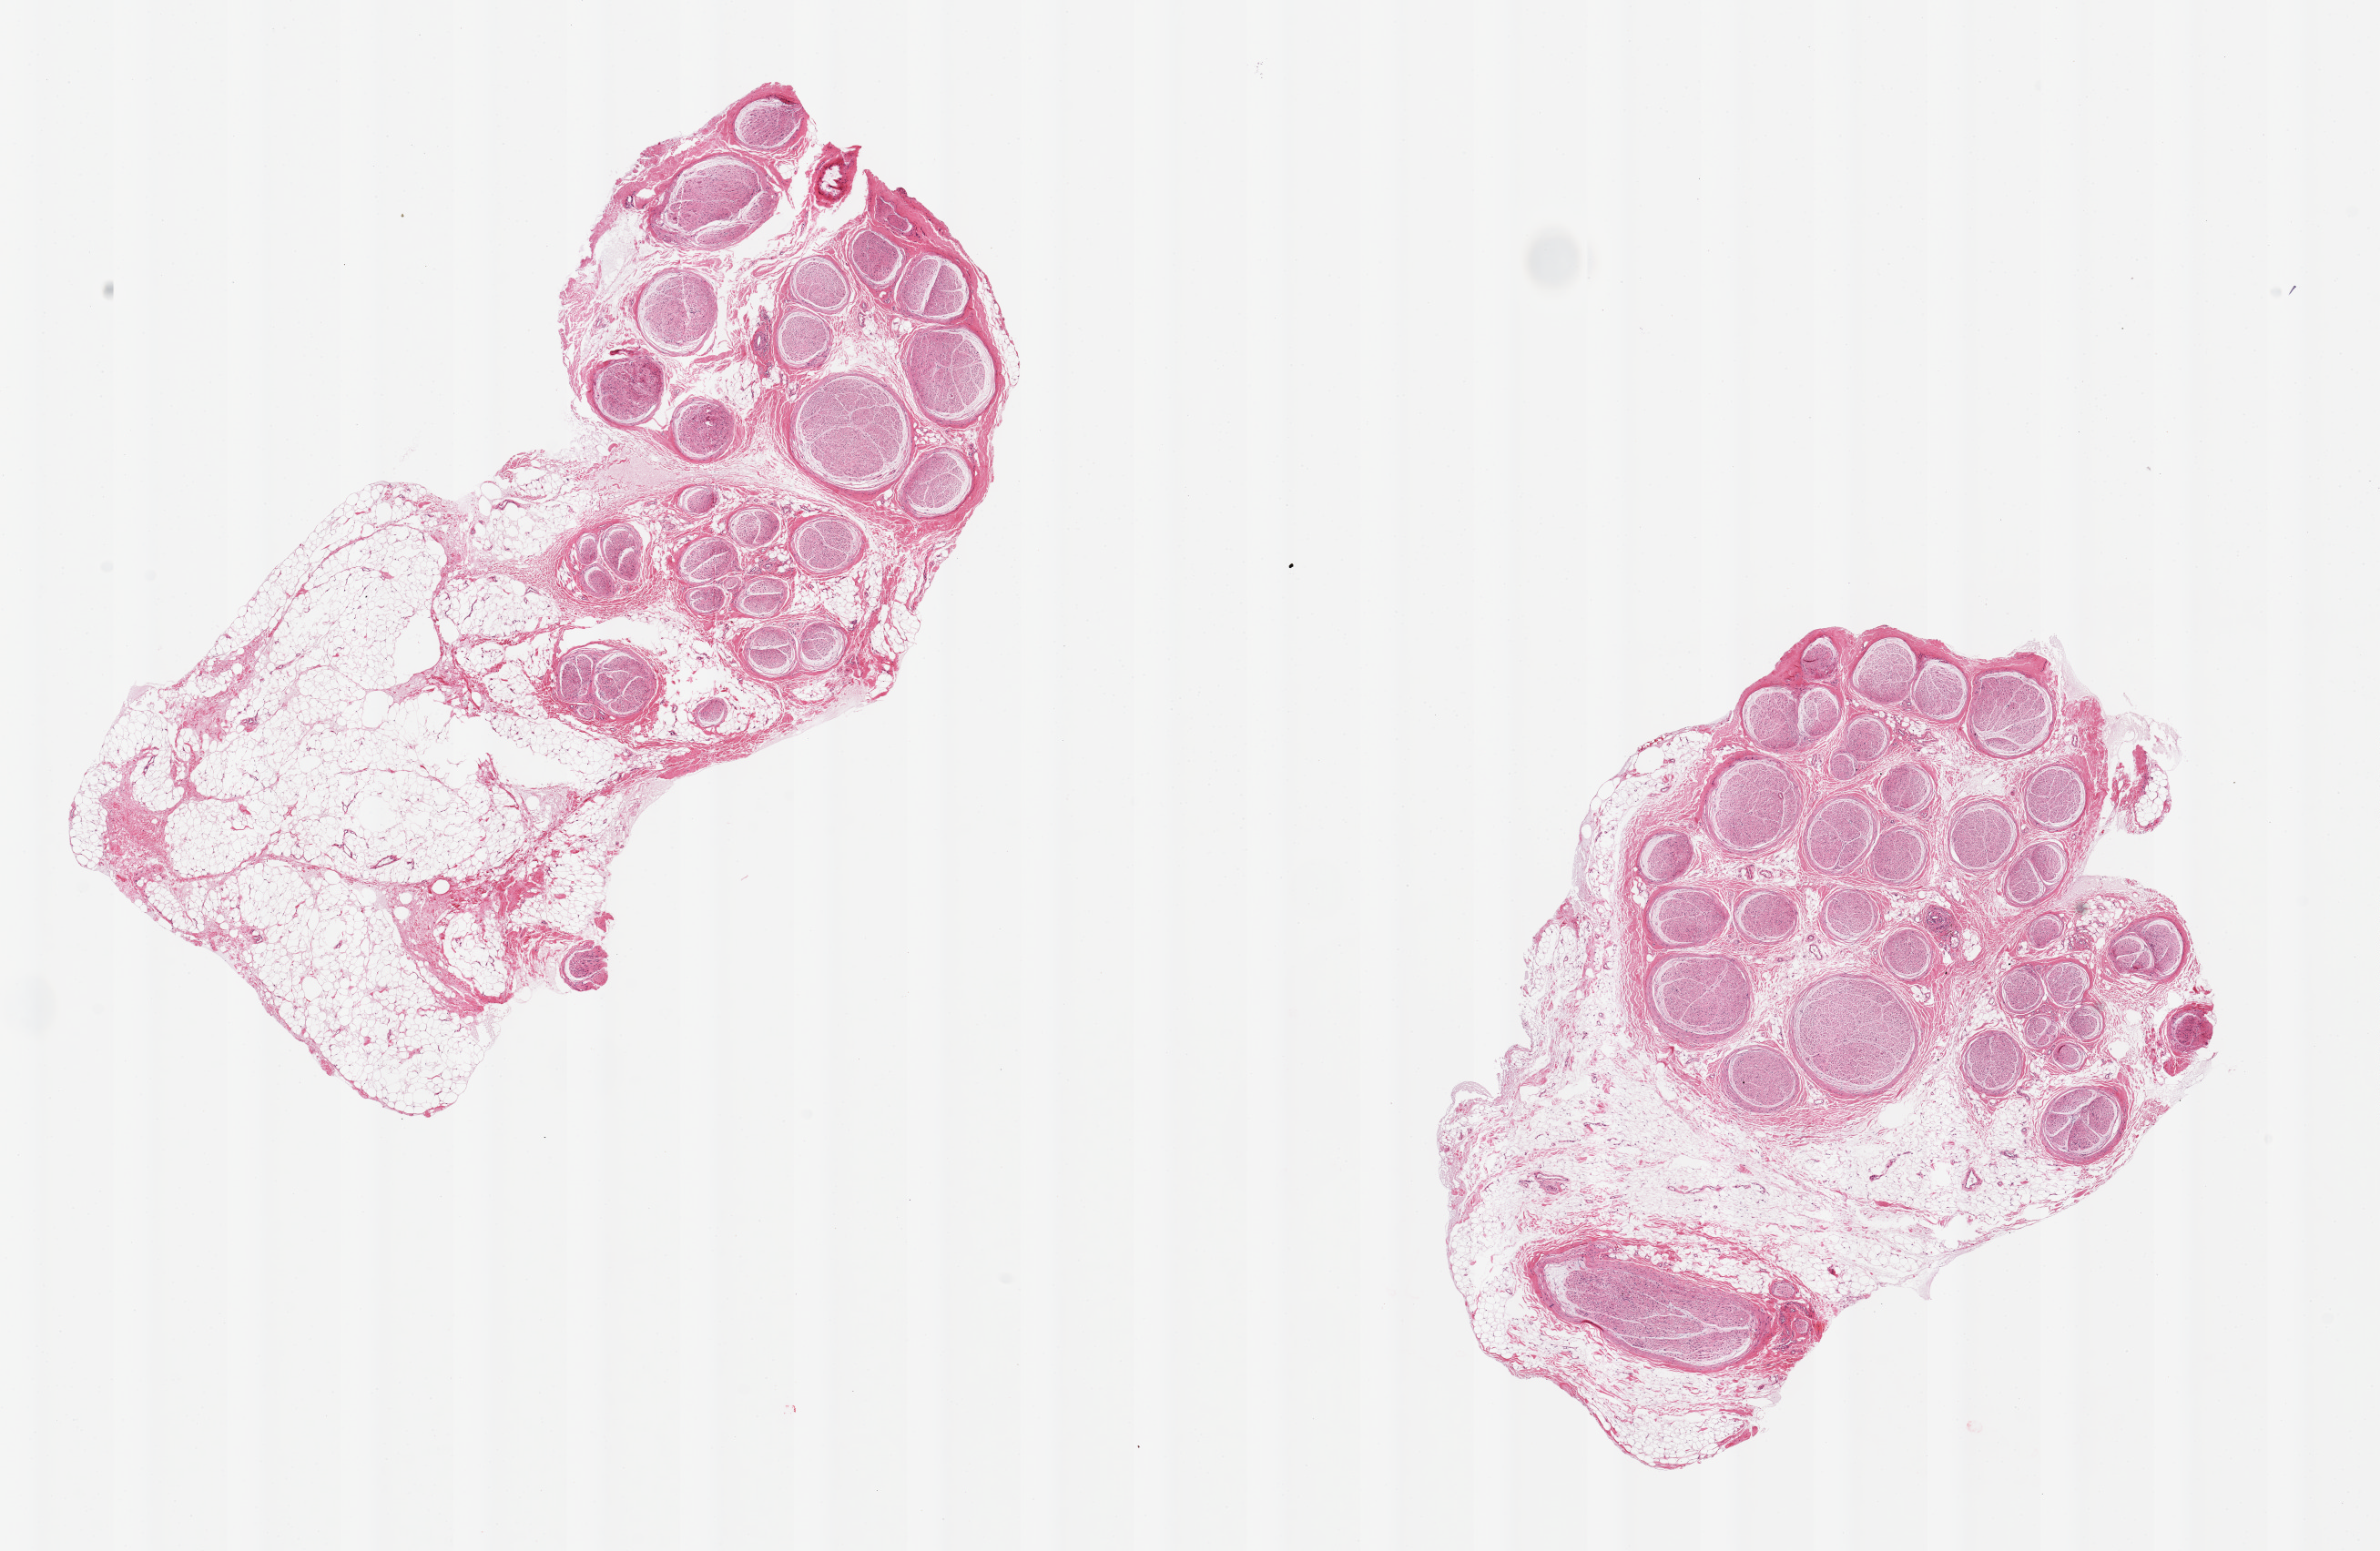
Haematoxylin and eosin whole-slide image, brightfield — low-resolution overview of the scanned area, about 20.7 x 13.5 mm (from a 20x scan); PAXgene-fixed, paraffin-embedded tissue; target tissue: tibial nerve; tissue donor sample. Female donor.
Pathologist's review note for this sample: 2 pieces, 9x5 & 8x5.5mm; 1 with 60% external adipose; 1 with 40% external adipose.